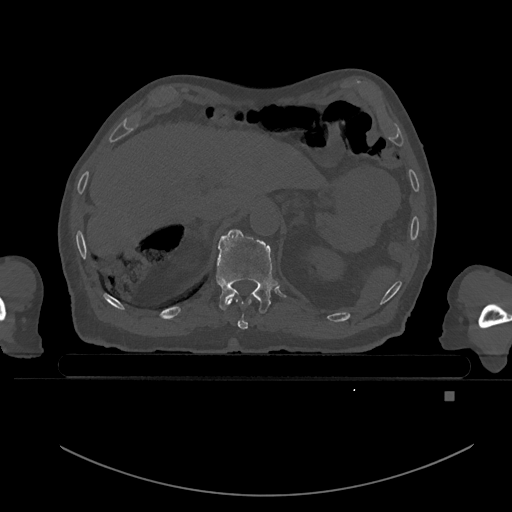
CT including the spine, one axial slice; position 47 of 969 along the scan axis; bone window (W 1800 / L 400 HU); 512 × 512 image matrix, field of view 456 × 456 mm. Patient: male, 82 years. Case-level facts recorded for this patient, not image findings: primary cancer: prostate; vertebrae with lytic lesions (as recorded): T11, T9, T8, T2.
Annotated regions visible in this slice (semi-automatically segmented with operator editing):
- T10 vertebra: bounding box (x1, y1, x2, y2) in pixels: (227, 298, 252, 330)
- T11 vertebra: (216, 229, 278, 314)